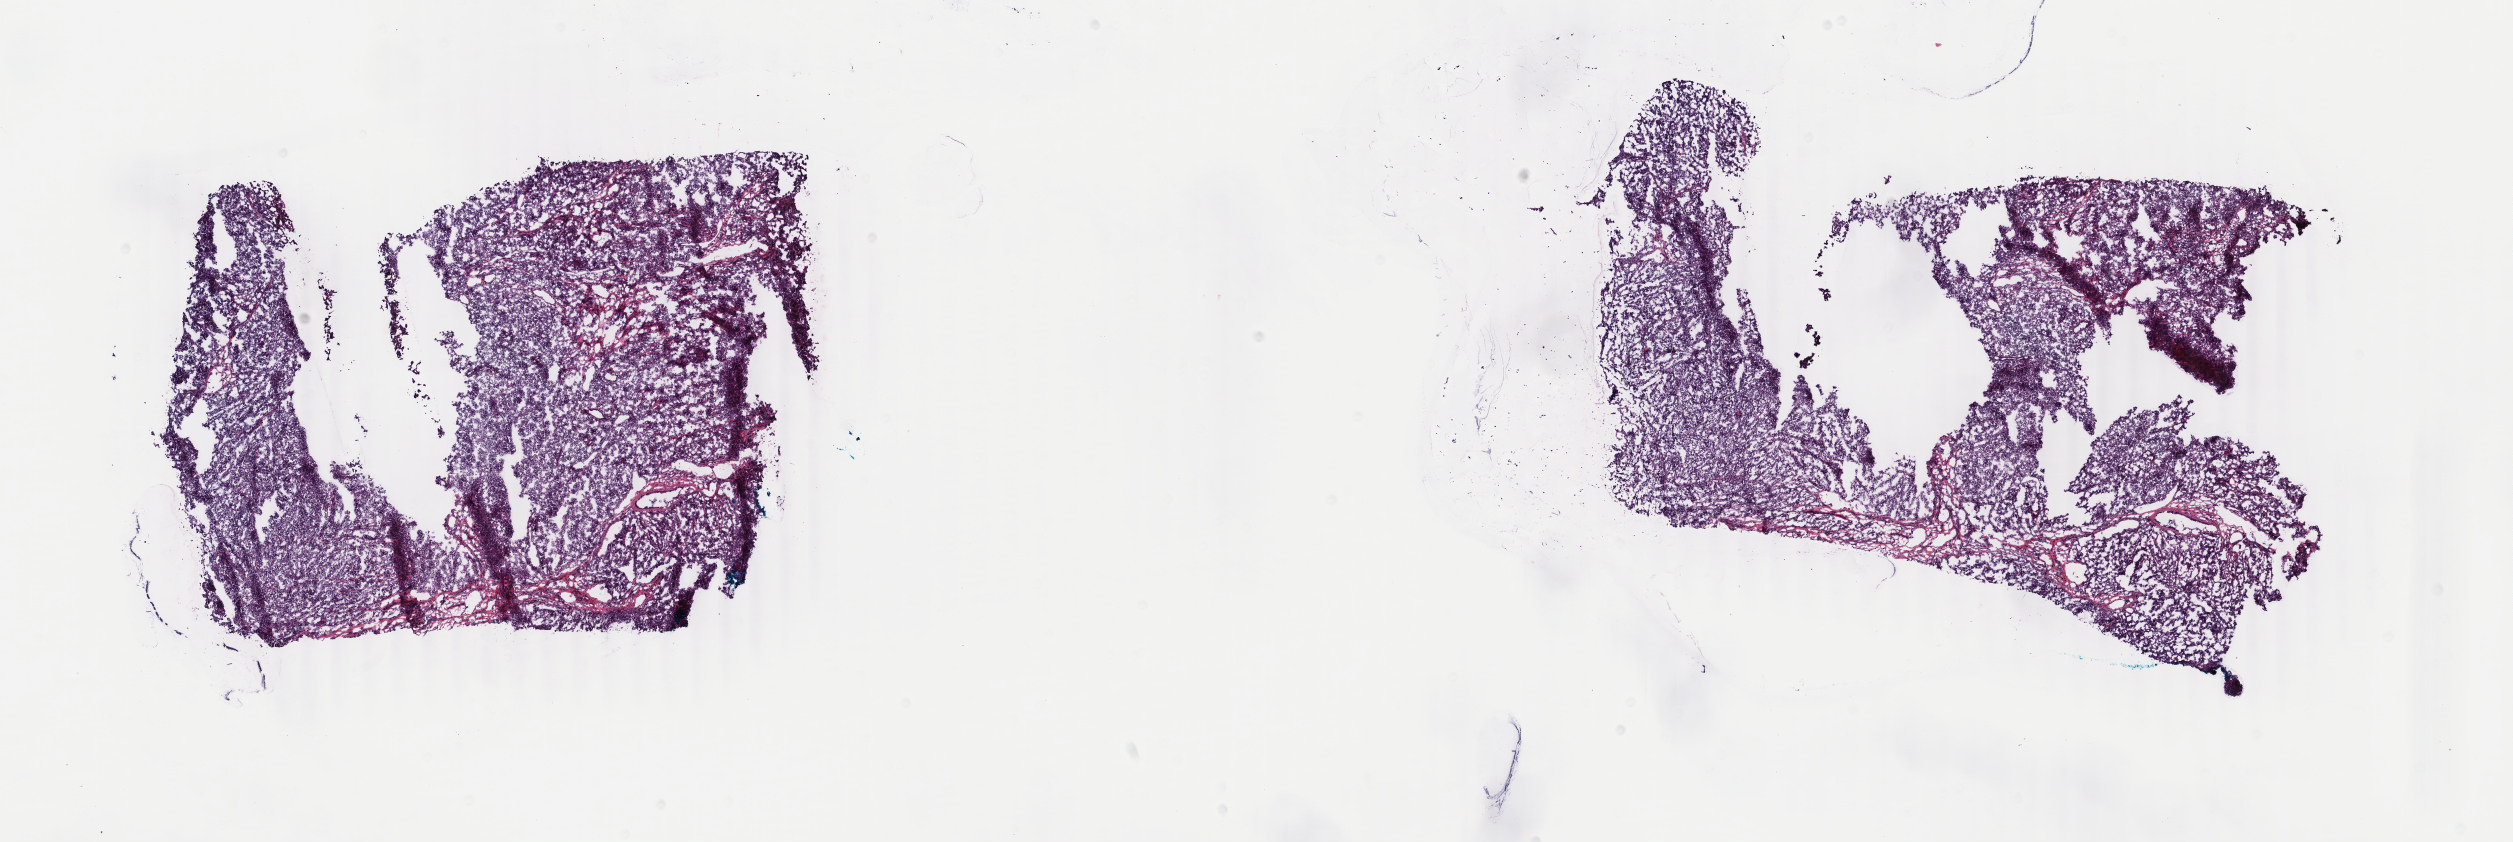
Whole-slide histology image, H&E-stained — shown as a low-resolution overview of the whole scanned area (about 20.0 x 6.7 mm), frozen section from the bottom of the tissue portion, primary tumour sample from the breast. Female patient; age at initial diagnosis 42 years. Slide review estimates, as recorded: tumour cells 95%, tumour nuclei 95%, normal cells 0%, stromal cells 4%, necrosis 1%. Infiltration values recorded for this section: lymphocyte infiltration 1%, monocyte infiltration 0%, neutrophil infiltration 0%.
- AJCC pathologic stage: IIB
- laterality: right
- lymph nodes positive (case pathology): 0 of 27 examined
- pathologic diagnosis: Infiltrating duct carcinoma, NOS